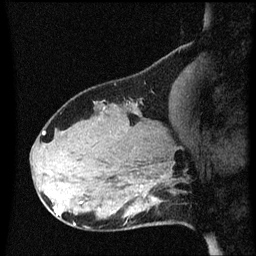
Breast MRI (dynamic contrast-enhanced), one sagittal slice. Slice 21 of 60 in the series (ordered by position). Dynamic contrast-enhanced series, image 2 of 3 at this slice position (ordered by acquisition). 1.5 T. TE 4.2 ms, TR 8.4 ms. 2 mm slice thickness. 256 × 256 image matrix, field of view 200 × 200 mm. Female patient, age 31 years. From the clinical record (not read from this slice): setting: breast cancer imaged before/during neoadjuvant chemotherapy; receptor status: HR-positive, HER2-negative.
Structures marked on this image (semi-automatic segmentation, software-assisted and operator-edited):
- analysis volume of interest (the breast-tissue region the enhancement analysis was run in; not a lesion): bounding box <102,166,176,229> (left, top, right, bottom; pixels)
- tumour enhancement mask (voxels above the 70 % enhancement threshold inside the analysis volume of interest): <152,198,155,201>